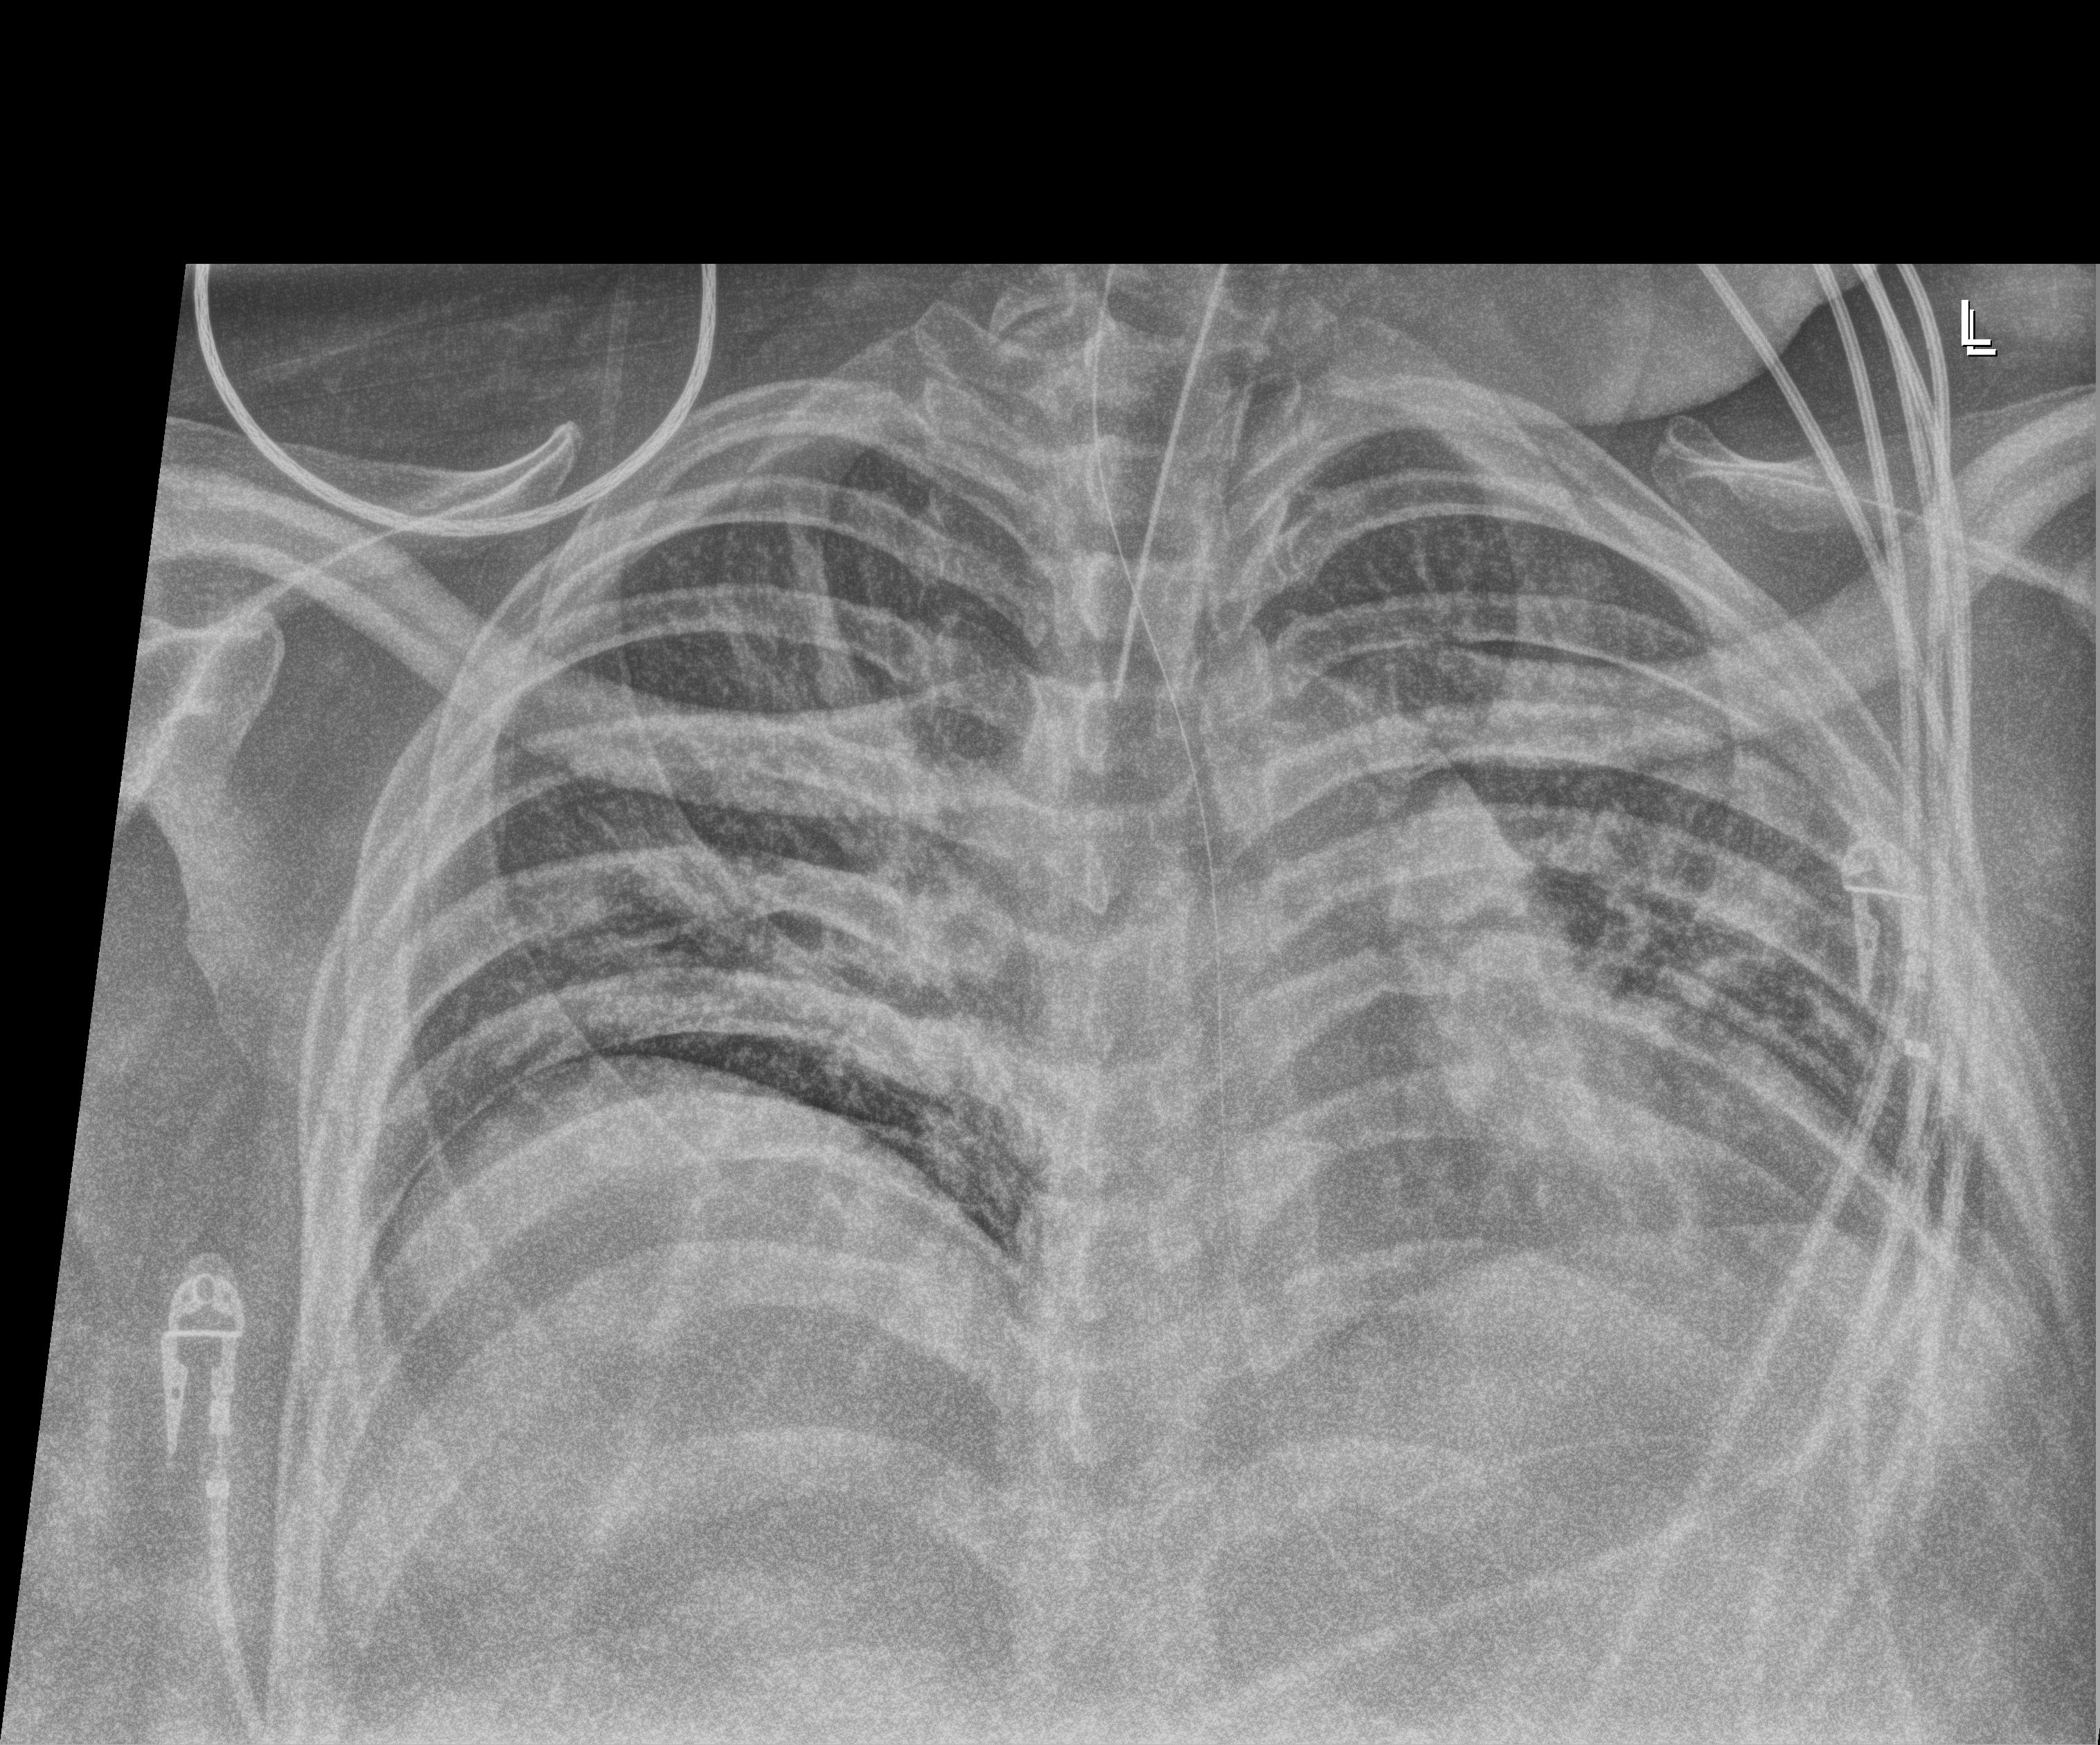
Chest X-ray (portable), anteroposterior (AP) projection. Patient hospitalised with COVID-19; male, aged 18–59 years.
From the hospital-stay record, not from the radiograph (when in the stay this image was taken is not recorded): admitted to intensive care during this hospital stay: yes; length of hospital stay: 69 days.